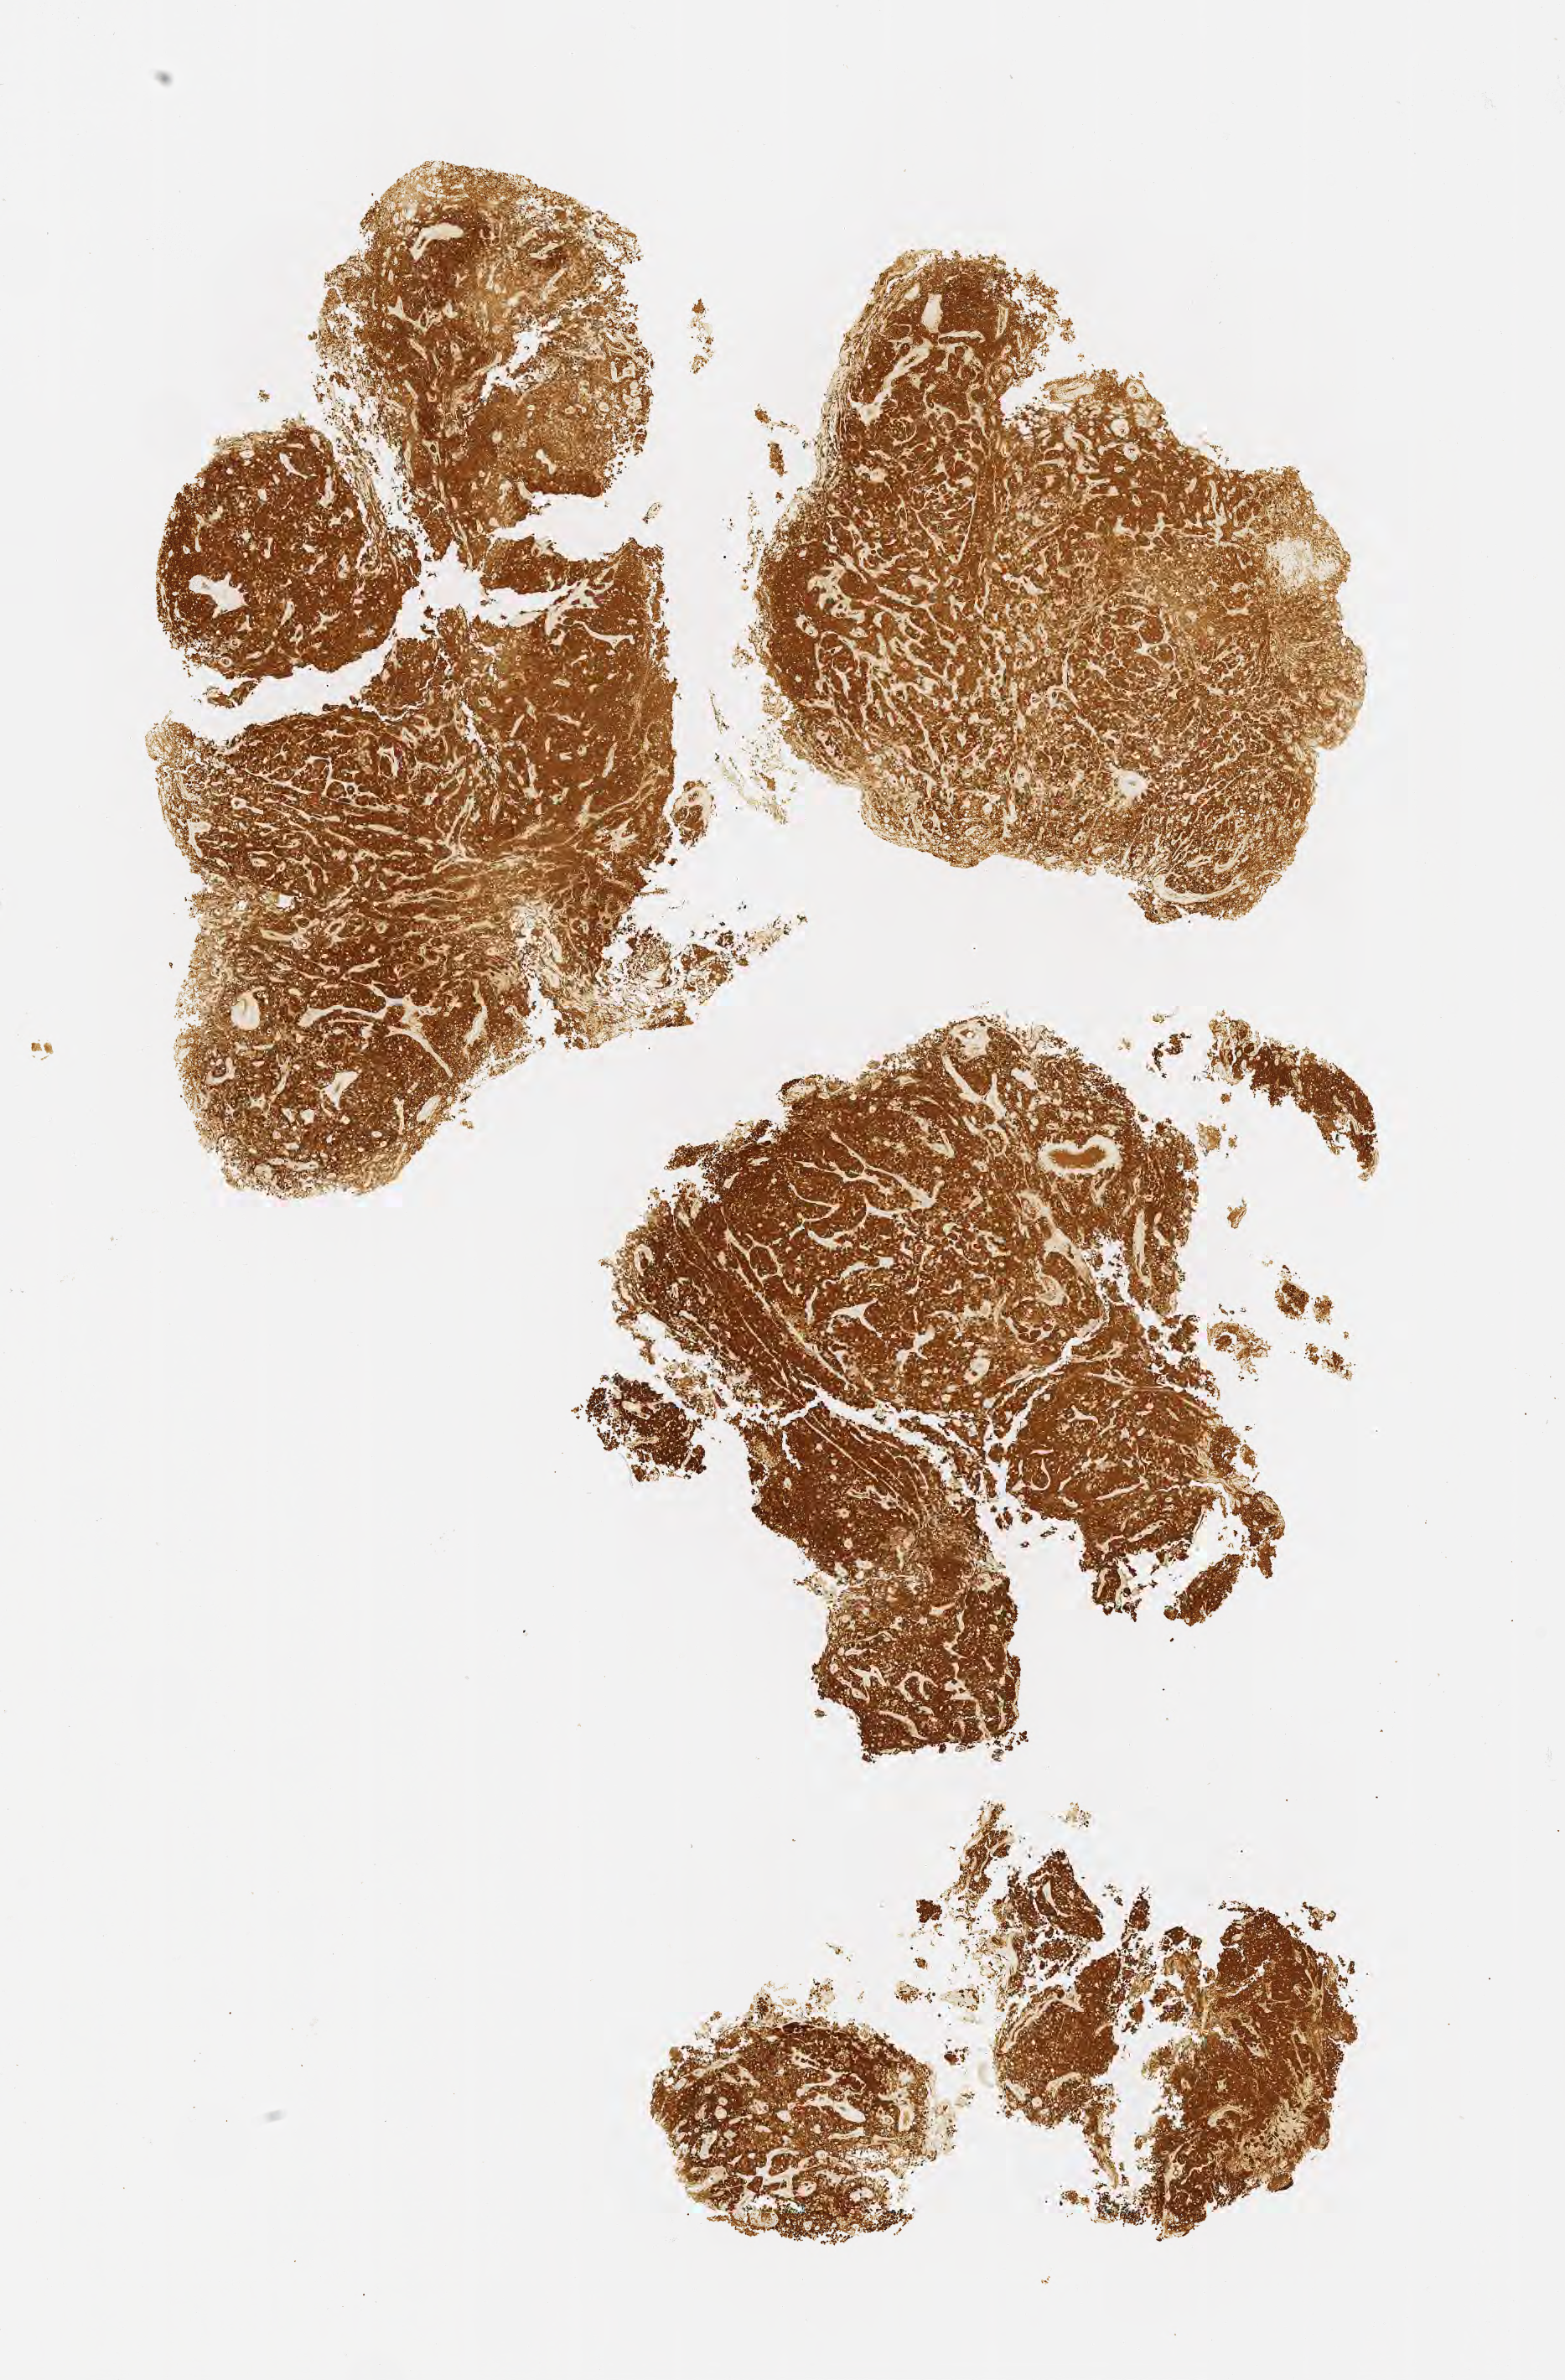
Immunohistochemistry (IHC) whole-slide image stained for p16 (p16INK4a) — a low-resolution overview of the entire scanned area, about 7.5 x 11.5 mm; specimen: tumor tissue; anatomic site: cervix. Patient female; 75 years old.
Histologic diagnosis: Adenocarcinoma, NOS.